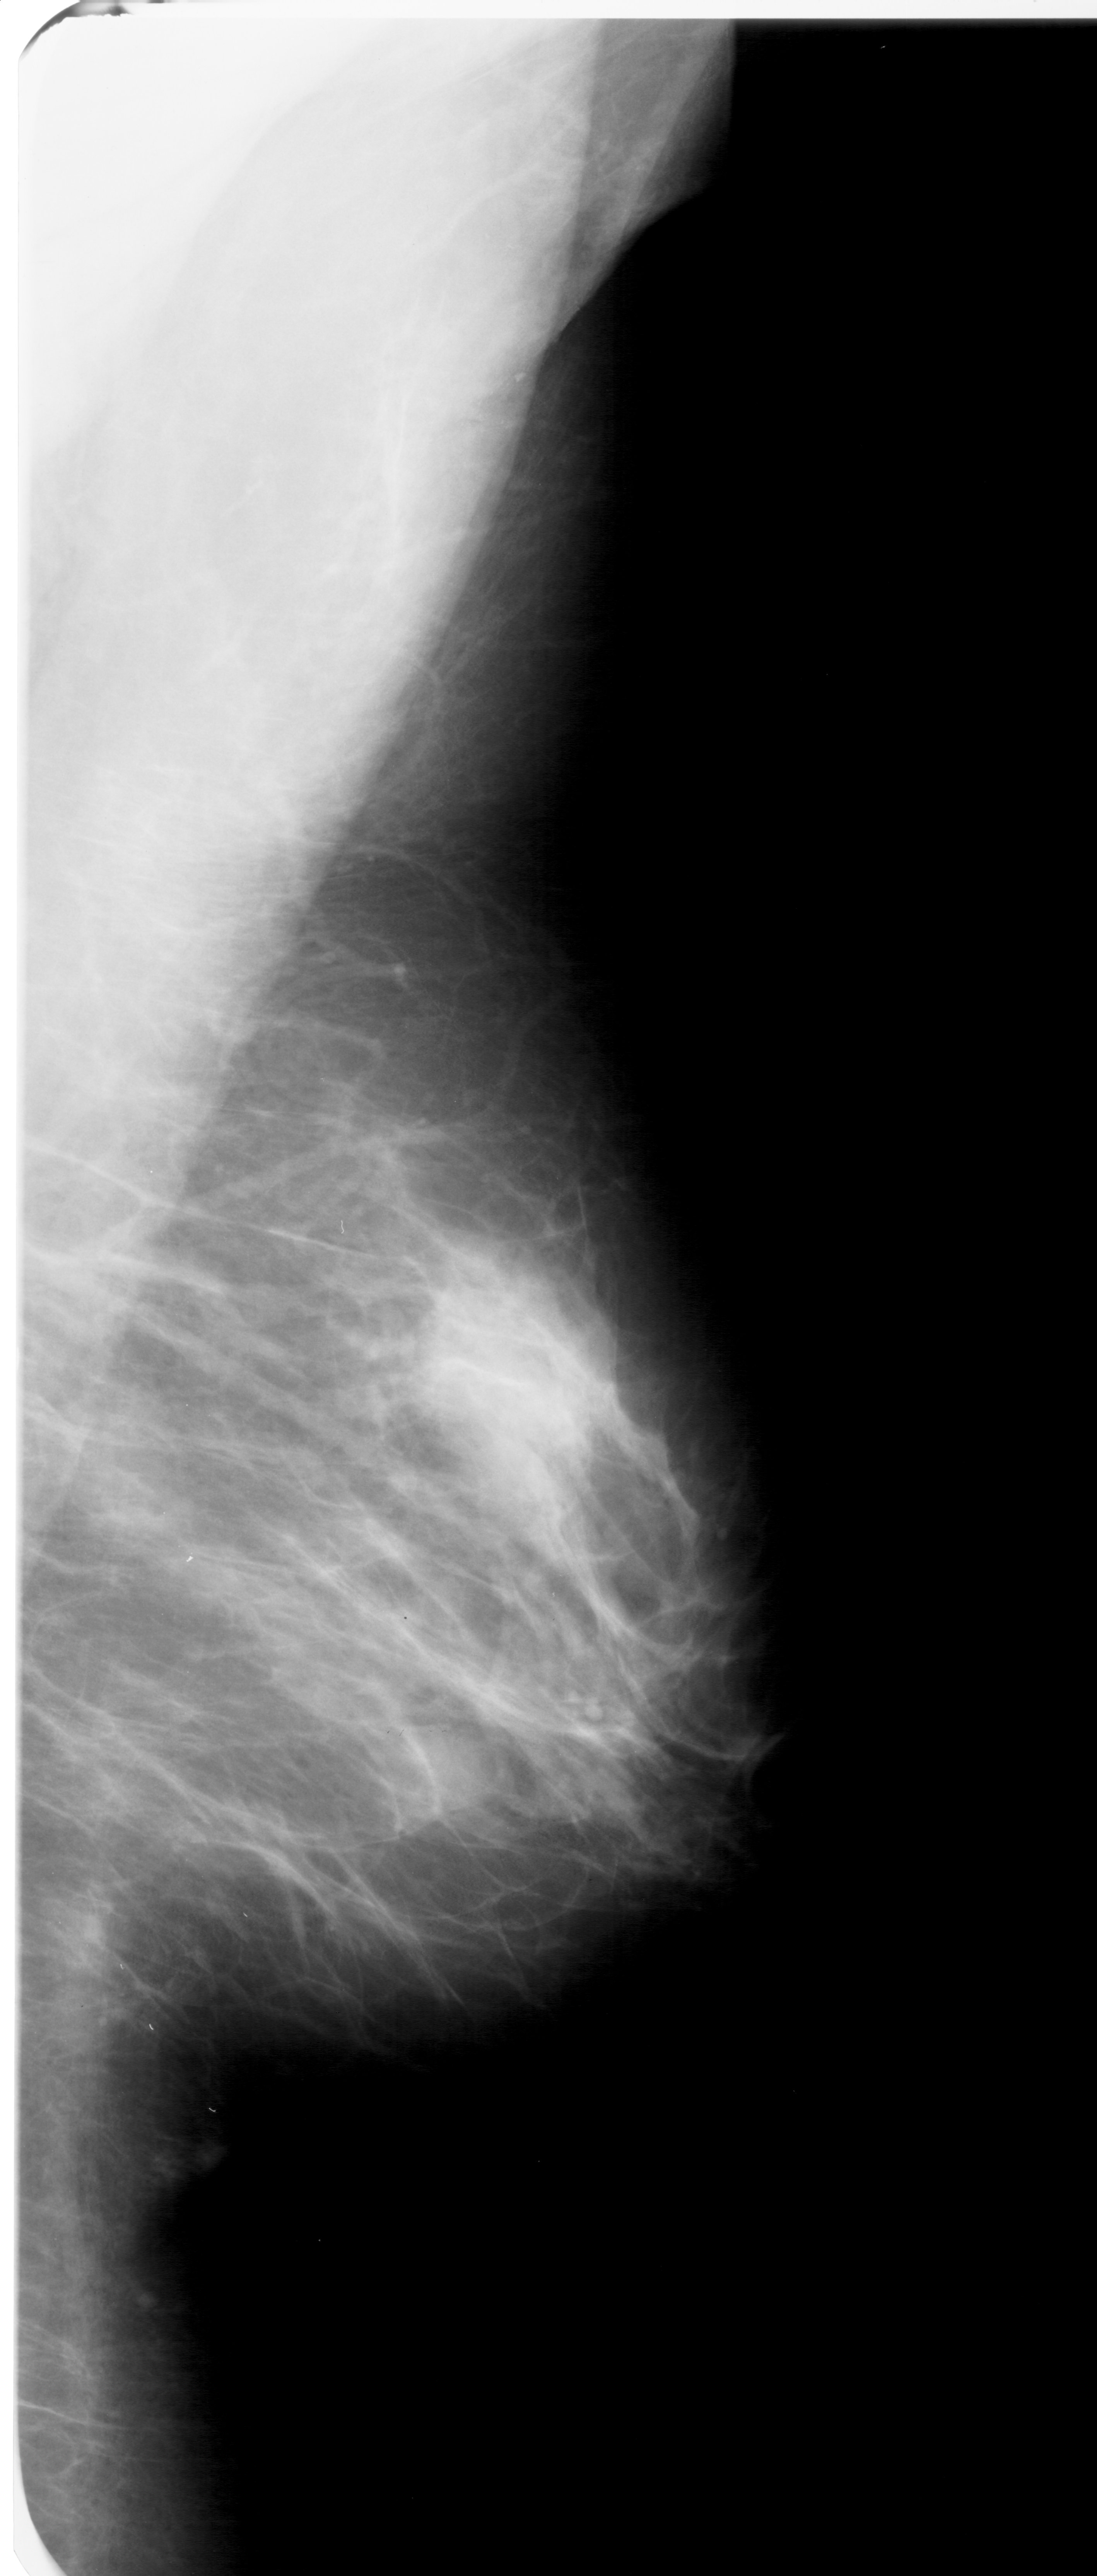
Mammogram (digitized film), right breast, mediolateral oblique (MLO) view, breast composition: almost entirely fatty (BI-RADS density category 1 of 4).
Abnormality record for this image: mass, shape oval, margins obscured; BI-RADS assessment category 3; pathology result (as recorded, not read from the image): benign.